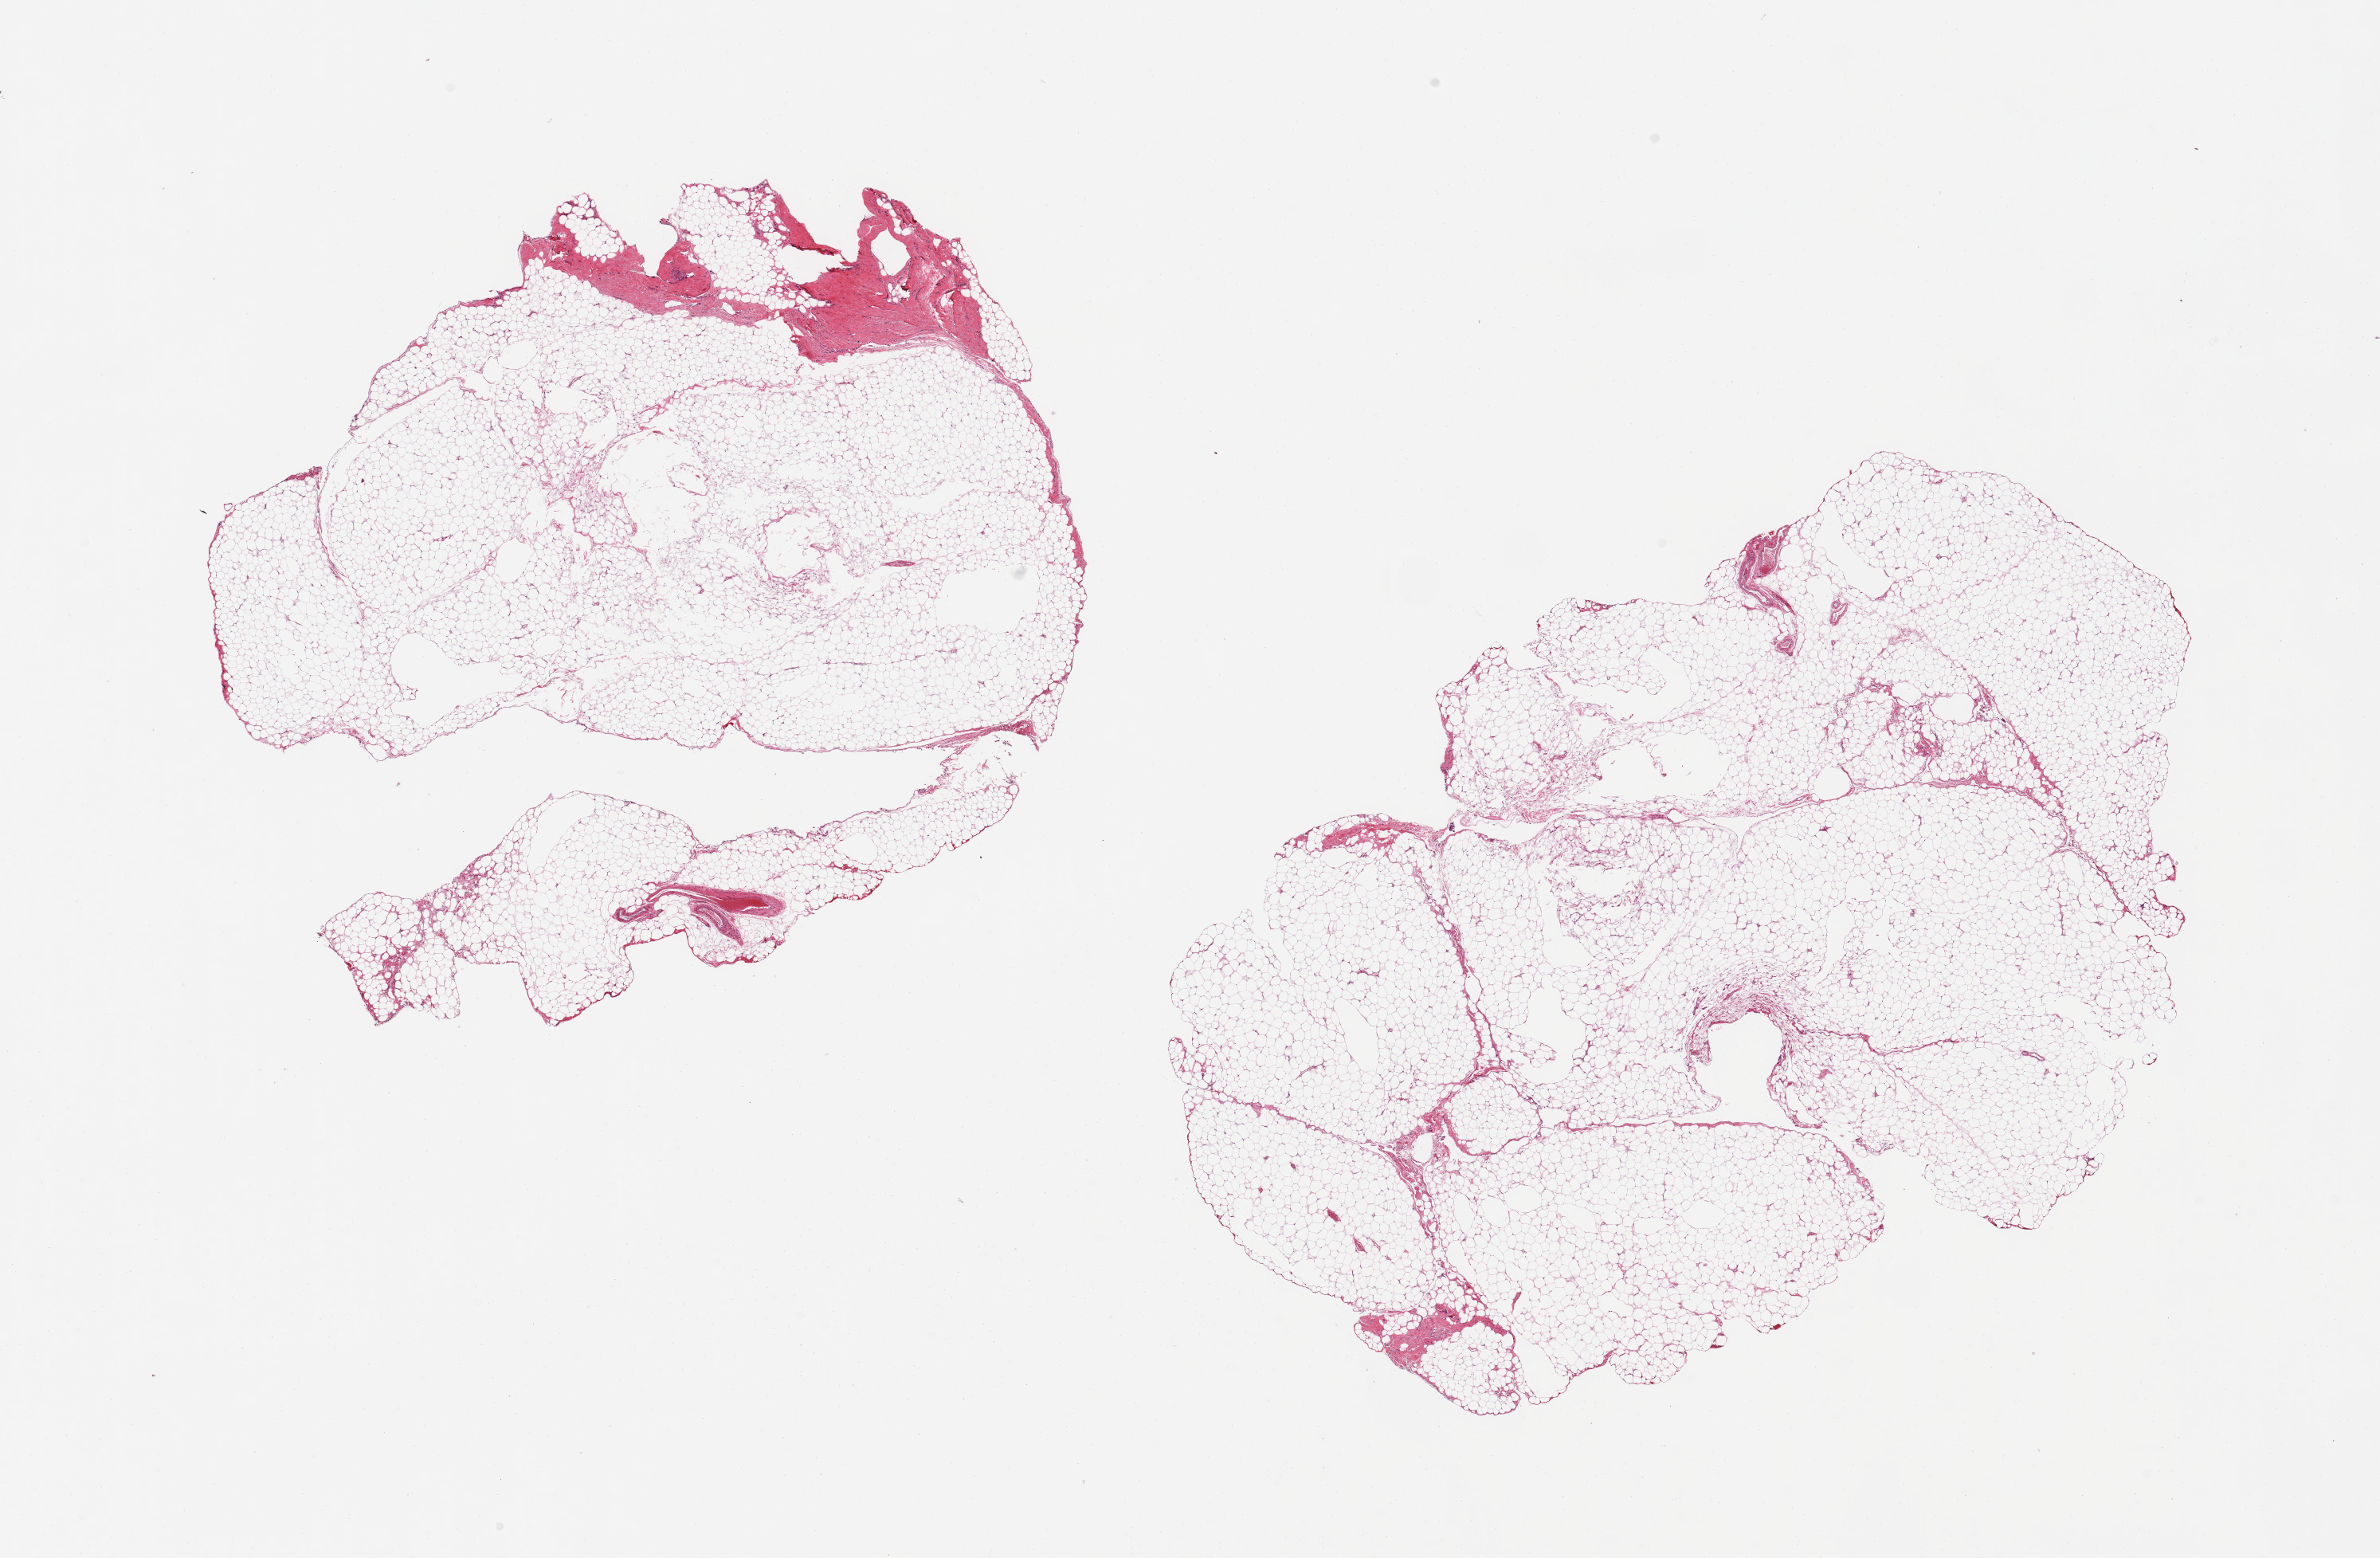
Whole-slide image, H&E stain, shown as a low-resolution overview of the whole scanned area (about 23.6 x 15.5 mm, from a 20x scan). PAXgene-fixed, paraffin-embedded tissue. Sampled site (target tissue): omentum. Donor tissue sample. Donor: male.
Pathologist's review note for this sample: 2 pieces; 10% fibrous content in 1 piece.